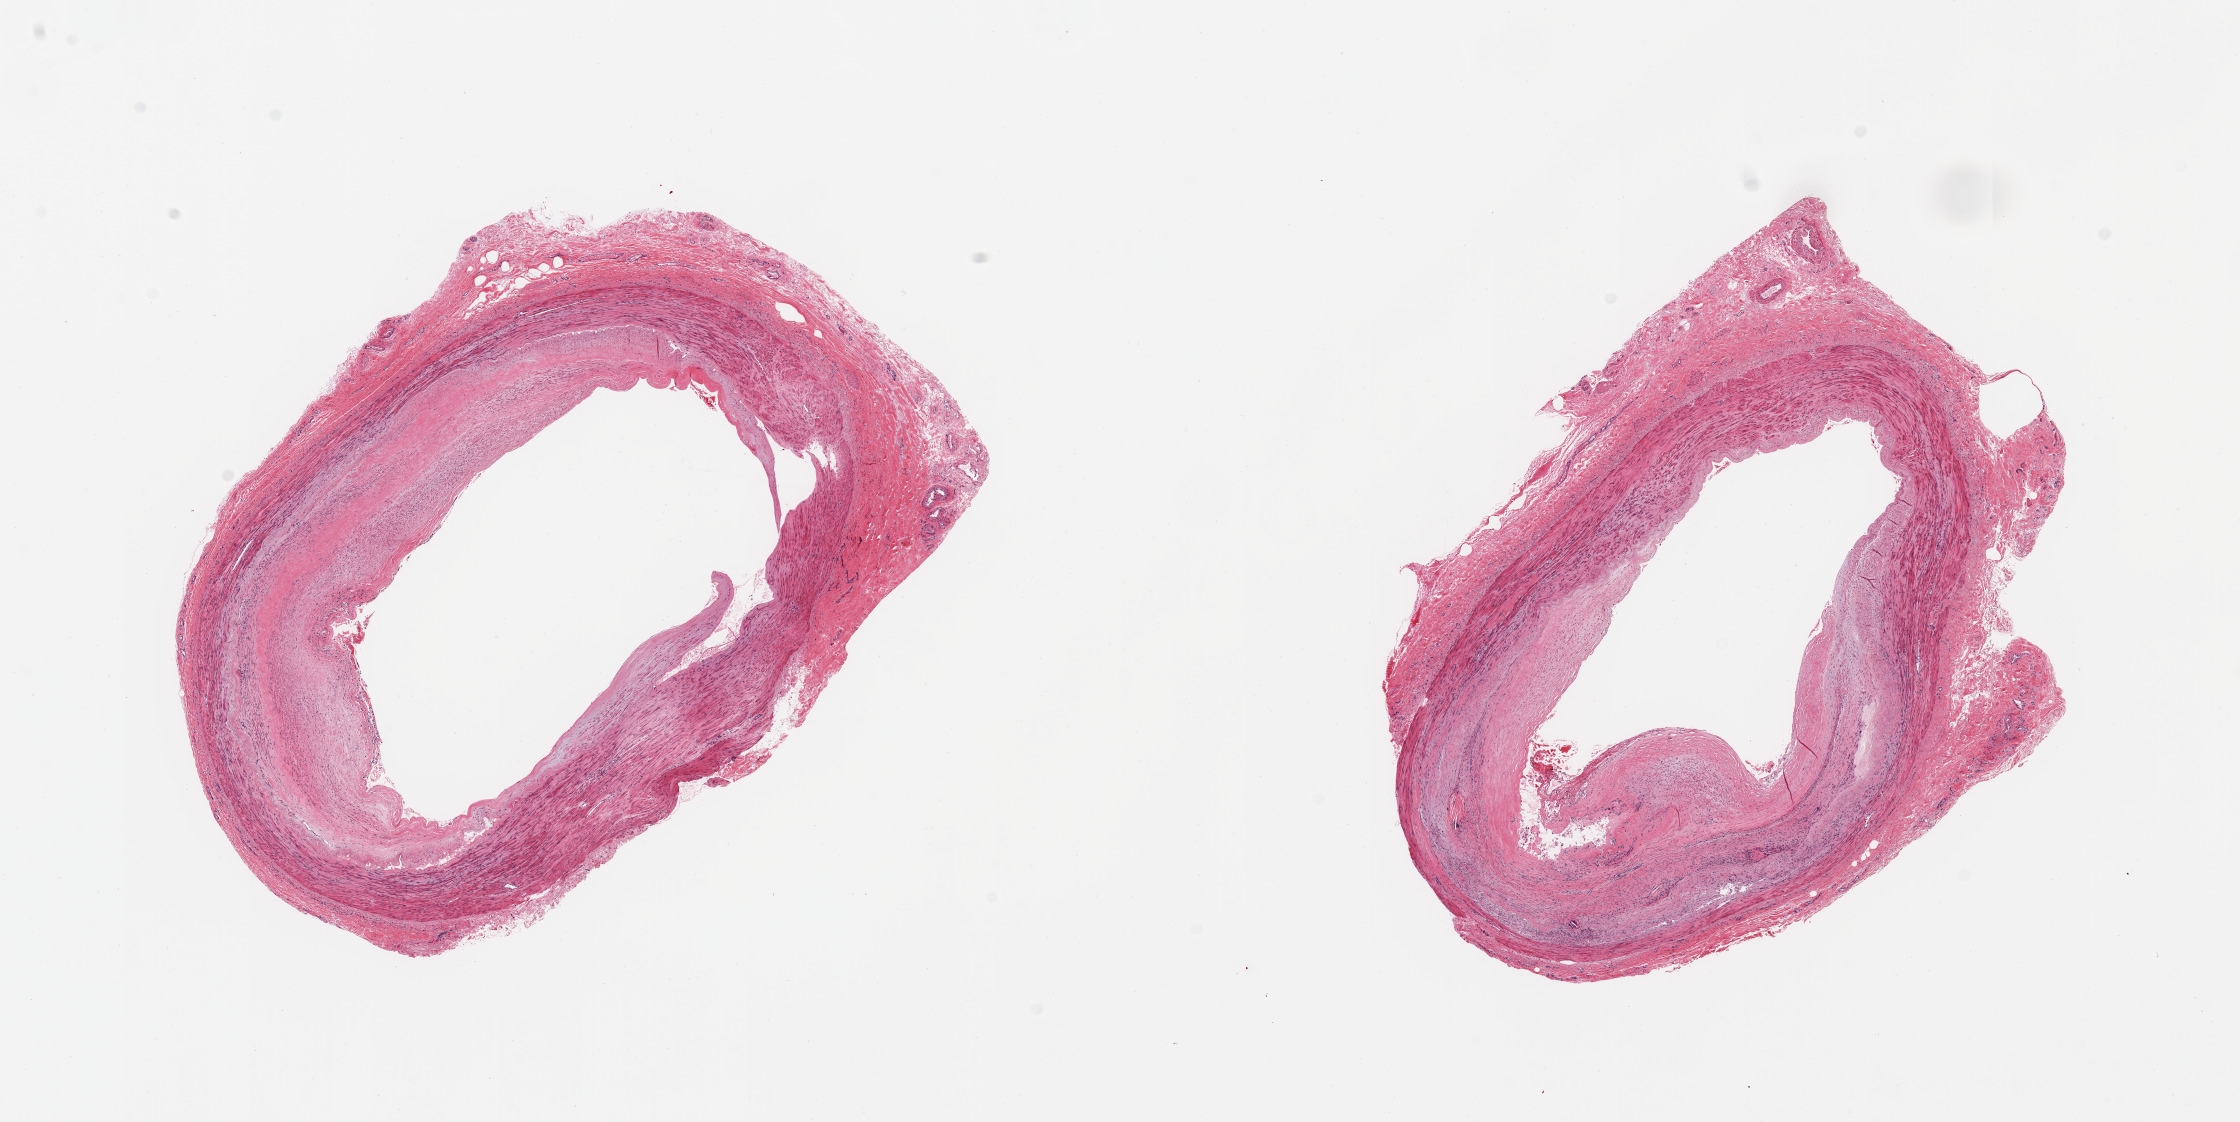
Whole-slide image, haematoxylin and eosin stain — a low-resolution overview of the entire scanned area, about 17.7 x 8.9 mm (from a 20x scan), PAXgene-fixed paraffin-embedded (PFPE) section, target tissue: tibial artery, tissue donor sample. Donor: male.
Review note (as recorded): 2 pieces; atherosclerosis.